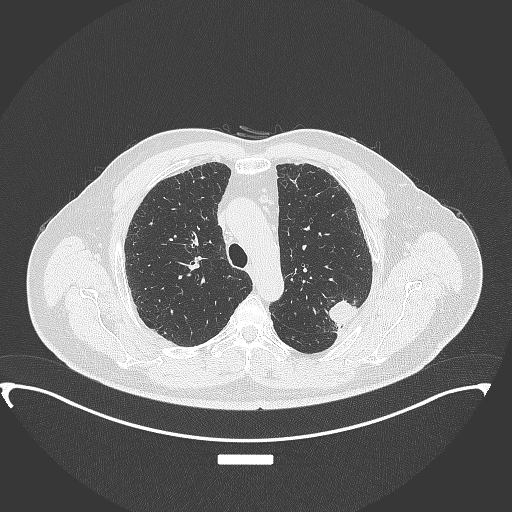
Chest CT, one axial slice. Reconstruction kernel B70f. 120 kVp. Lung window (W 1500 / L -600 HU). 512 × 512 image matrix. Male patient, age 64 years. From the clinical record (not read from this slice): clinical TNM (as recorded): T1c N1 M1.
Structures marked on this image (bounding box drawn by a radiologist):
- lung tumour (recorded histology: adenocarcinoma): box from (x=321, y=295) to (x=365, y=333) px